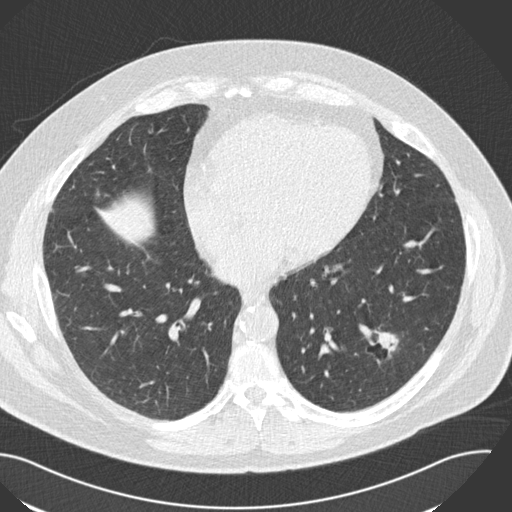
Low-dose screening chest CT, one axial slice; position 72 of 153 along the scan axis; 120 kVp; lung window (W 1500 / L -600 HU); 512 × 512 image matrix, field of view 394 × 394 mm.
Outlined on this slice (outlined manually by an expert reader):
- lesion 1 (tumor, lower lobe of left lung): box from (x=374, y=330) to (x=398, y=363) px